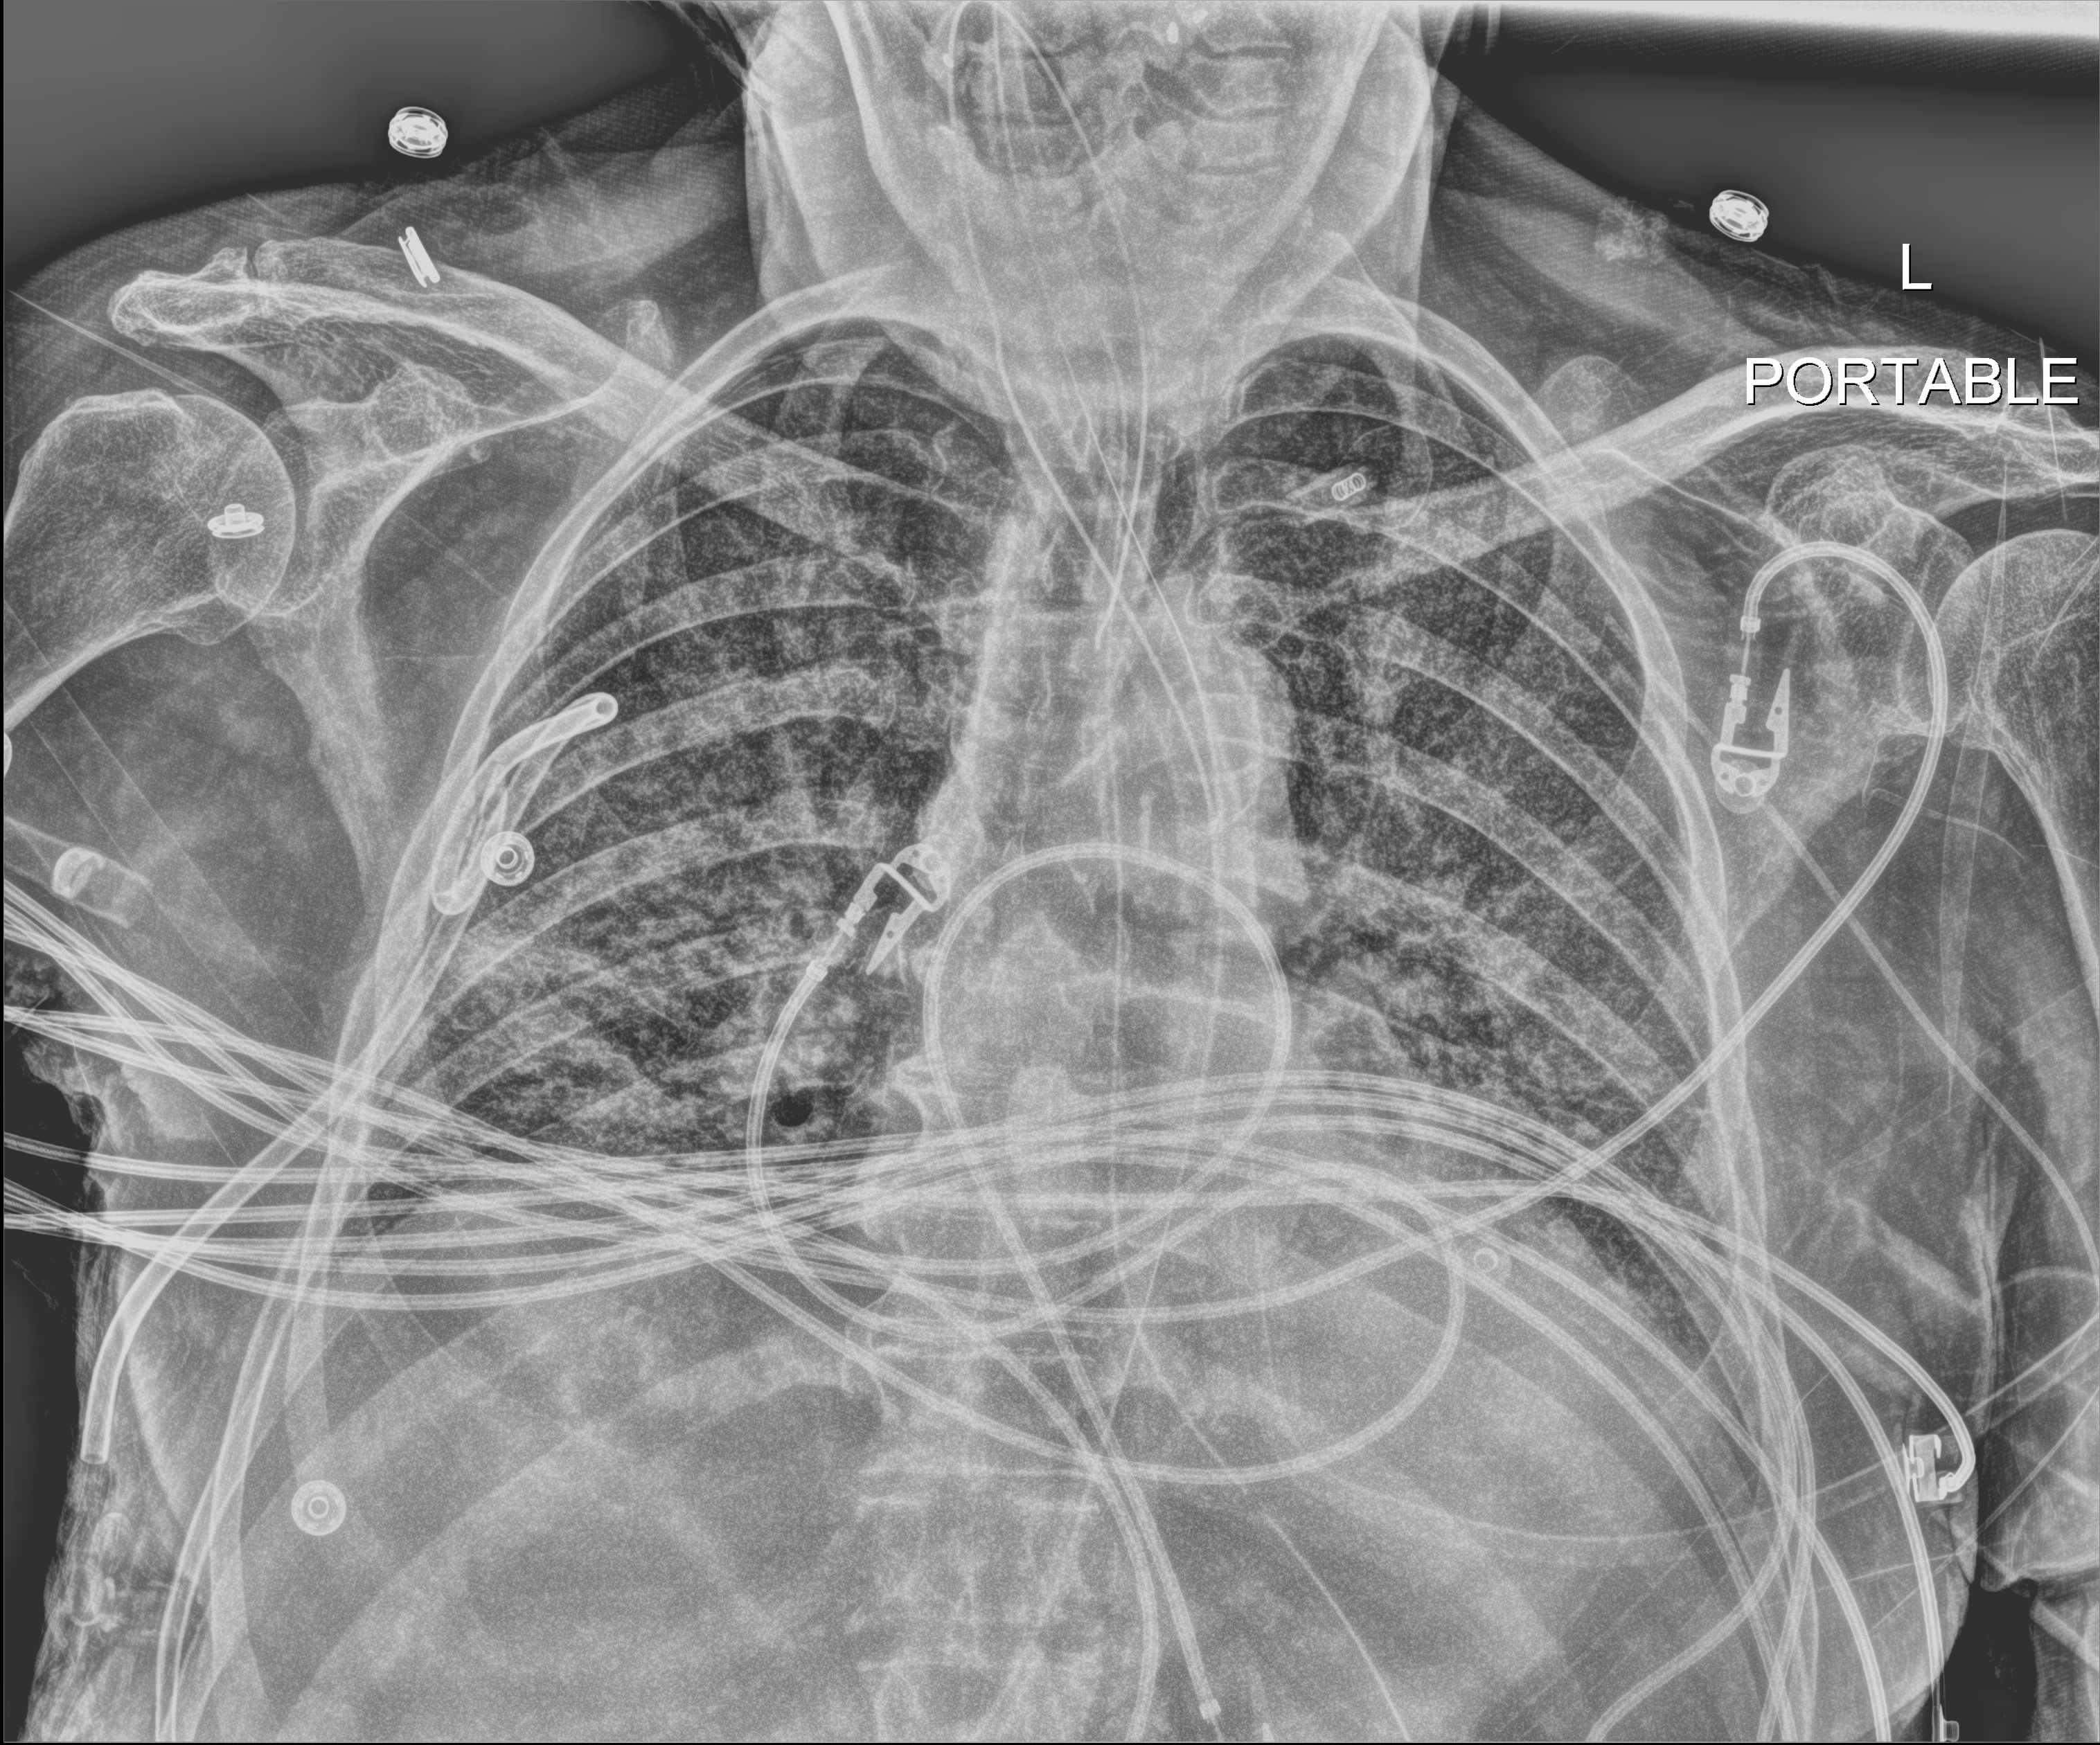
Bedside chest radiograph (digital radiography). Patient hospitalised with COVID-19; male, aged 75–90 years.
Hospital-stay facts (about this admission, not read from this image; timing relative to this image not recorded):
- smoking status (admission record): never
- admitted to intensive care during this hospital stay: yes